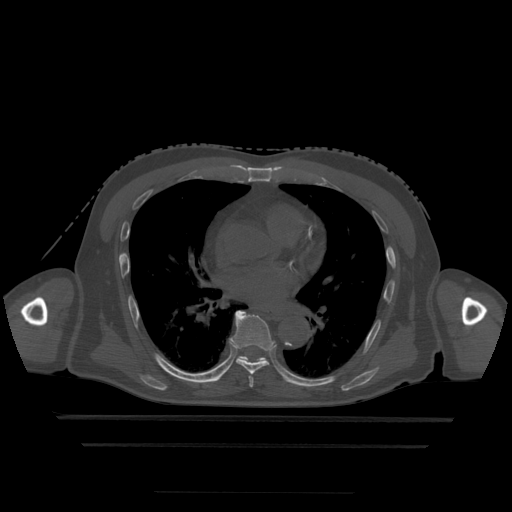
CT including the spine, one axial slice. Position 296 of 522 along the scan axis. Bone window (W 1800 / L 400 HU). 1.25 mm slice thickness. 512 × 512 image matrix, field of view 436 × 436 mm. Patient age 68 years. From the clinical record (not read from this slice): primary cancer: urothelial.
Outlined on this slice (semi-automatically segmented with operator editing):
- T6 vertebra: bounding box [x1, y1, x2, y2] px = [249, 377, 254, 388]
- T7 vertebra: [230, 311, 275, 375]
- T8 vertebra: [238, 356, 267, 363]